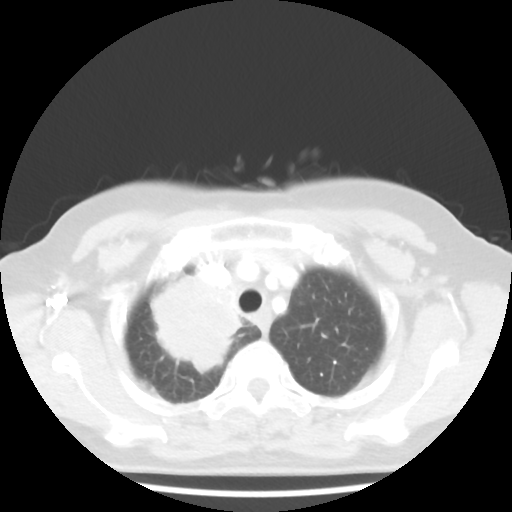
Chest CT, one axial slice; 100 kVp; lung window (W 1500 / L -600 HU); 5 mm slice thickness; 512 × 512 image matrix. Female patient, age 62 years. Case-level facts recorded for this patient, not image findings: clinical TNM (as recorded): T3 N0 M0; histopathological grade: G3.
Annotated regions visible in this slice (bounding box drawn by a radiologist):
- lung tumour (recorded histology: small cell carcinoma): box from (x=139, y=267) to (x=254, y=384) px